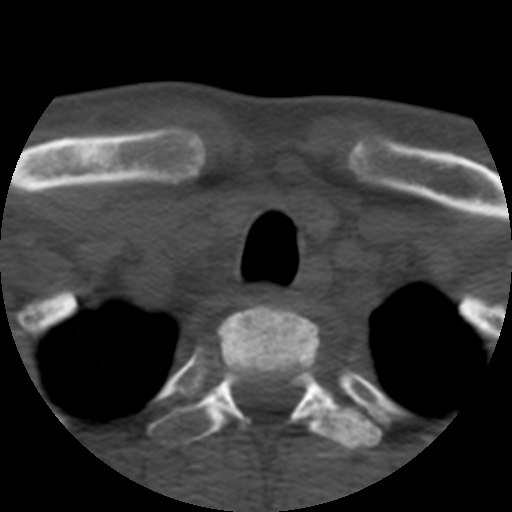
CT including the spine, one axial slice. Position 438 of 508 along the scan axis. Bone window (W 1800 / L 400 HU). 1.25 mm slice thickness. 512 × 512 image matrix, field of view 160 × 160 mm. Patient age 57 years. Case-level facts recorded for this patient, not image findings: primary cancer: prostate.
Structures marked on this image (semi-automatically segmented with operator editing):
- T1 vertebra: bounding box (x1, y1, x2, y2) in pixels: (218, 305, 320, 380)
- T2 vertebra: (146, 360, 382, 454)